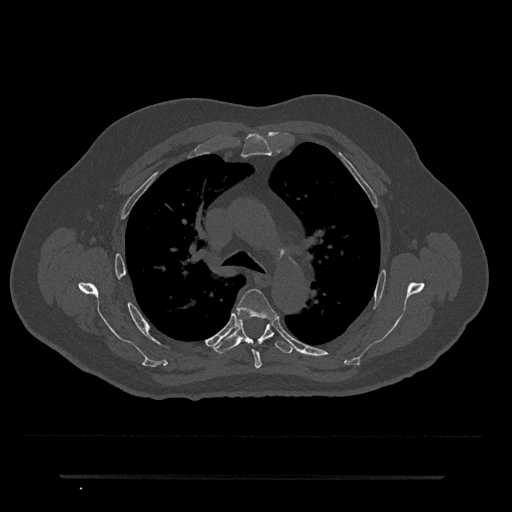
CT including the spine, one axial slice; position 504 of 797 along the scan axis; reconstruction kernel Br40s/3; bone window (W 1800 / L 400 HU); 0.5 mm slice thickness; 512 × 512 image matrix. Patient: male, 69 years. From the clinical record (not read from this slice): primary cancer: prostate.
Structures marked on this image (semi-automatically segmented with operator editing):
- T4 vertebra: bounding box [x1, y1, x2, y2] px = [237, 288, 277, 369]
- T5 vertebra: [212, 319, 294, 354]